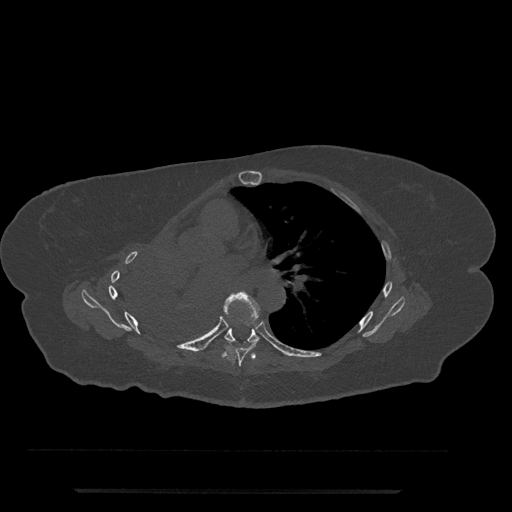
CT including the spine, one axial slice; slice 471 of 797 in the series (ordered by position); reconstruction kernel Br40s/3; 120 kVp; bone window (W 1800 / L 400 HU); 512 × 512 image matrix. Patient: female, 51 years. From the clinical record (not read from this slice): primary cancer: neuro; vertebrae with lytic lesions (as recorded): T8.
Structures marked on this image (semi-automatically segmented with operator editing):
- T6 vertebra: box from (x=223, y=291) to (x=260, y=367) px
- T7 vertebra: (x=224, y=328)–(x=260, y=343)